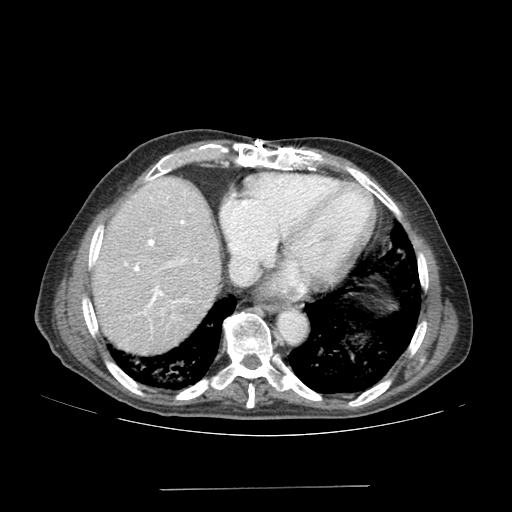
Contrast-enhanced abdominal CT (liver protocol), one axial slice. Slice 150 of 192 in the series (ordered by position). Reconstruction kernel SOFT. Soft-tissue window (W 400 / L 40 HU). 2.5 mm slice thickness. 512 × 512 image matrix. Case-level facts recorded for this patient, not image findings: diagnosis: hepatocellular carcinoma (patient treated with transarterial chemoembolisation; whether this scan precedes or follows treatment is not stated here); TNM stage (as recorded): Stage-IVA; Child-Pugh class: A; tumour nodularity: uninodular.
Outlined on this slice (semi-automatically segmented with operator editing):
- abdominal aorta: box from (x=279, y=313) to (x=304, y=342) px
- liver parenchyma outside the tumour (the mass and vessels are separate outlines, so this box may not span the whole liver): (x=92, y=176)–(x=220, y=354)
- liver vessels: (x=124, y=176)–(x=196, y=318)